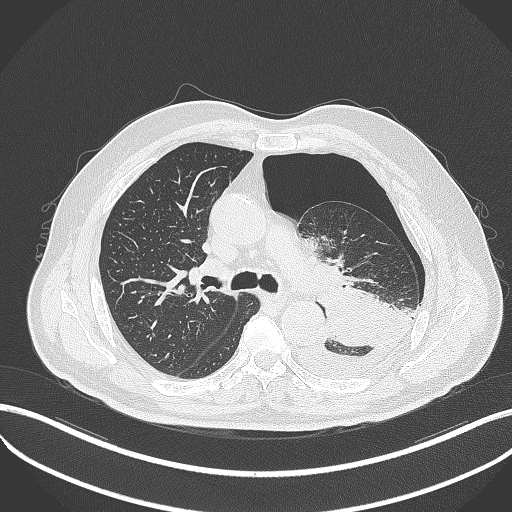
Chest CT, one axial slice; position 332 of 464 along the scan axis; reconstruction kernel B70f; 120 kVp; lung window (W 1500 / L -600 HU); 512 × 512 image matrix, field of view 400 × 400 mm. Male patient, age 76 years. Case-level facts recorded for this patient, not image findings: clinical TNM (as recorded): T3 N0 M1b.
Structures marked on this image (rectangle marked by the reading radiologist):
- lung tumour (recorded histology: adenocarcinoma): bounding box [x1, y1, x2, y2] px = [319, 288, 399, 348]